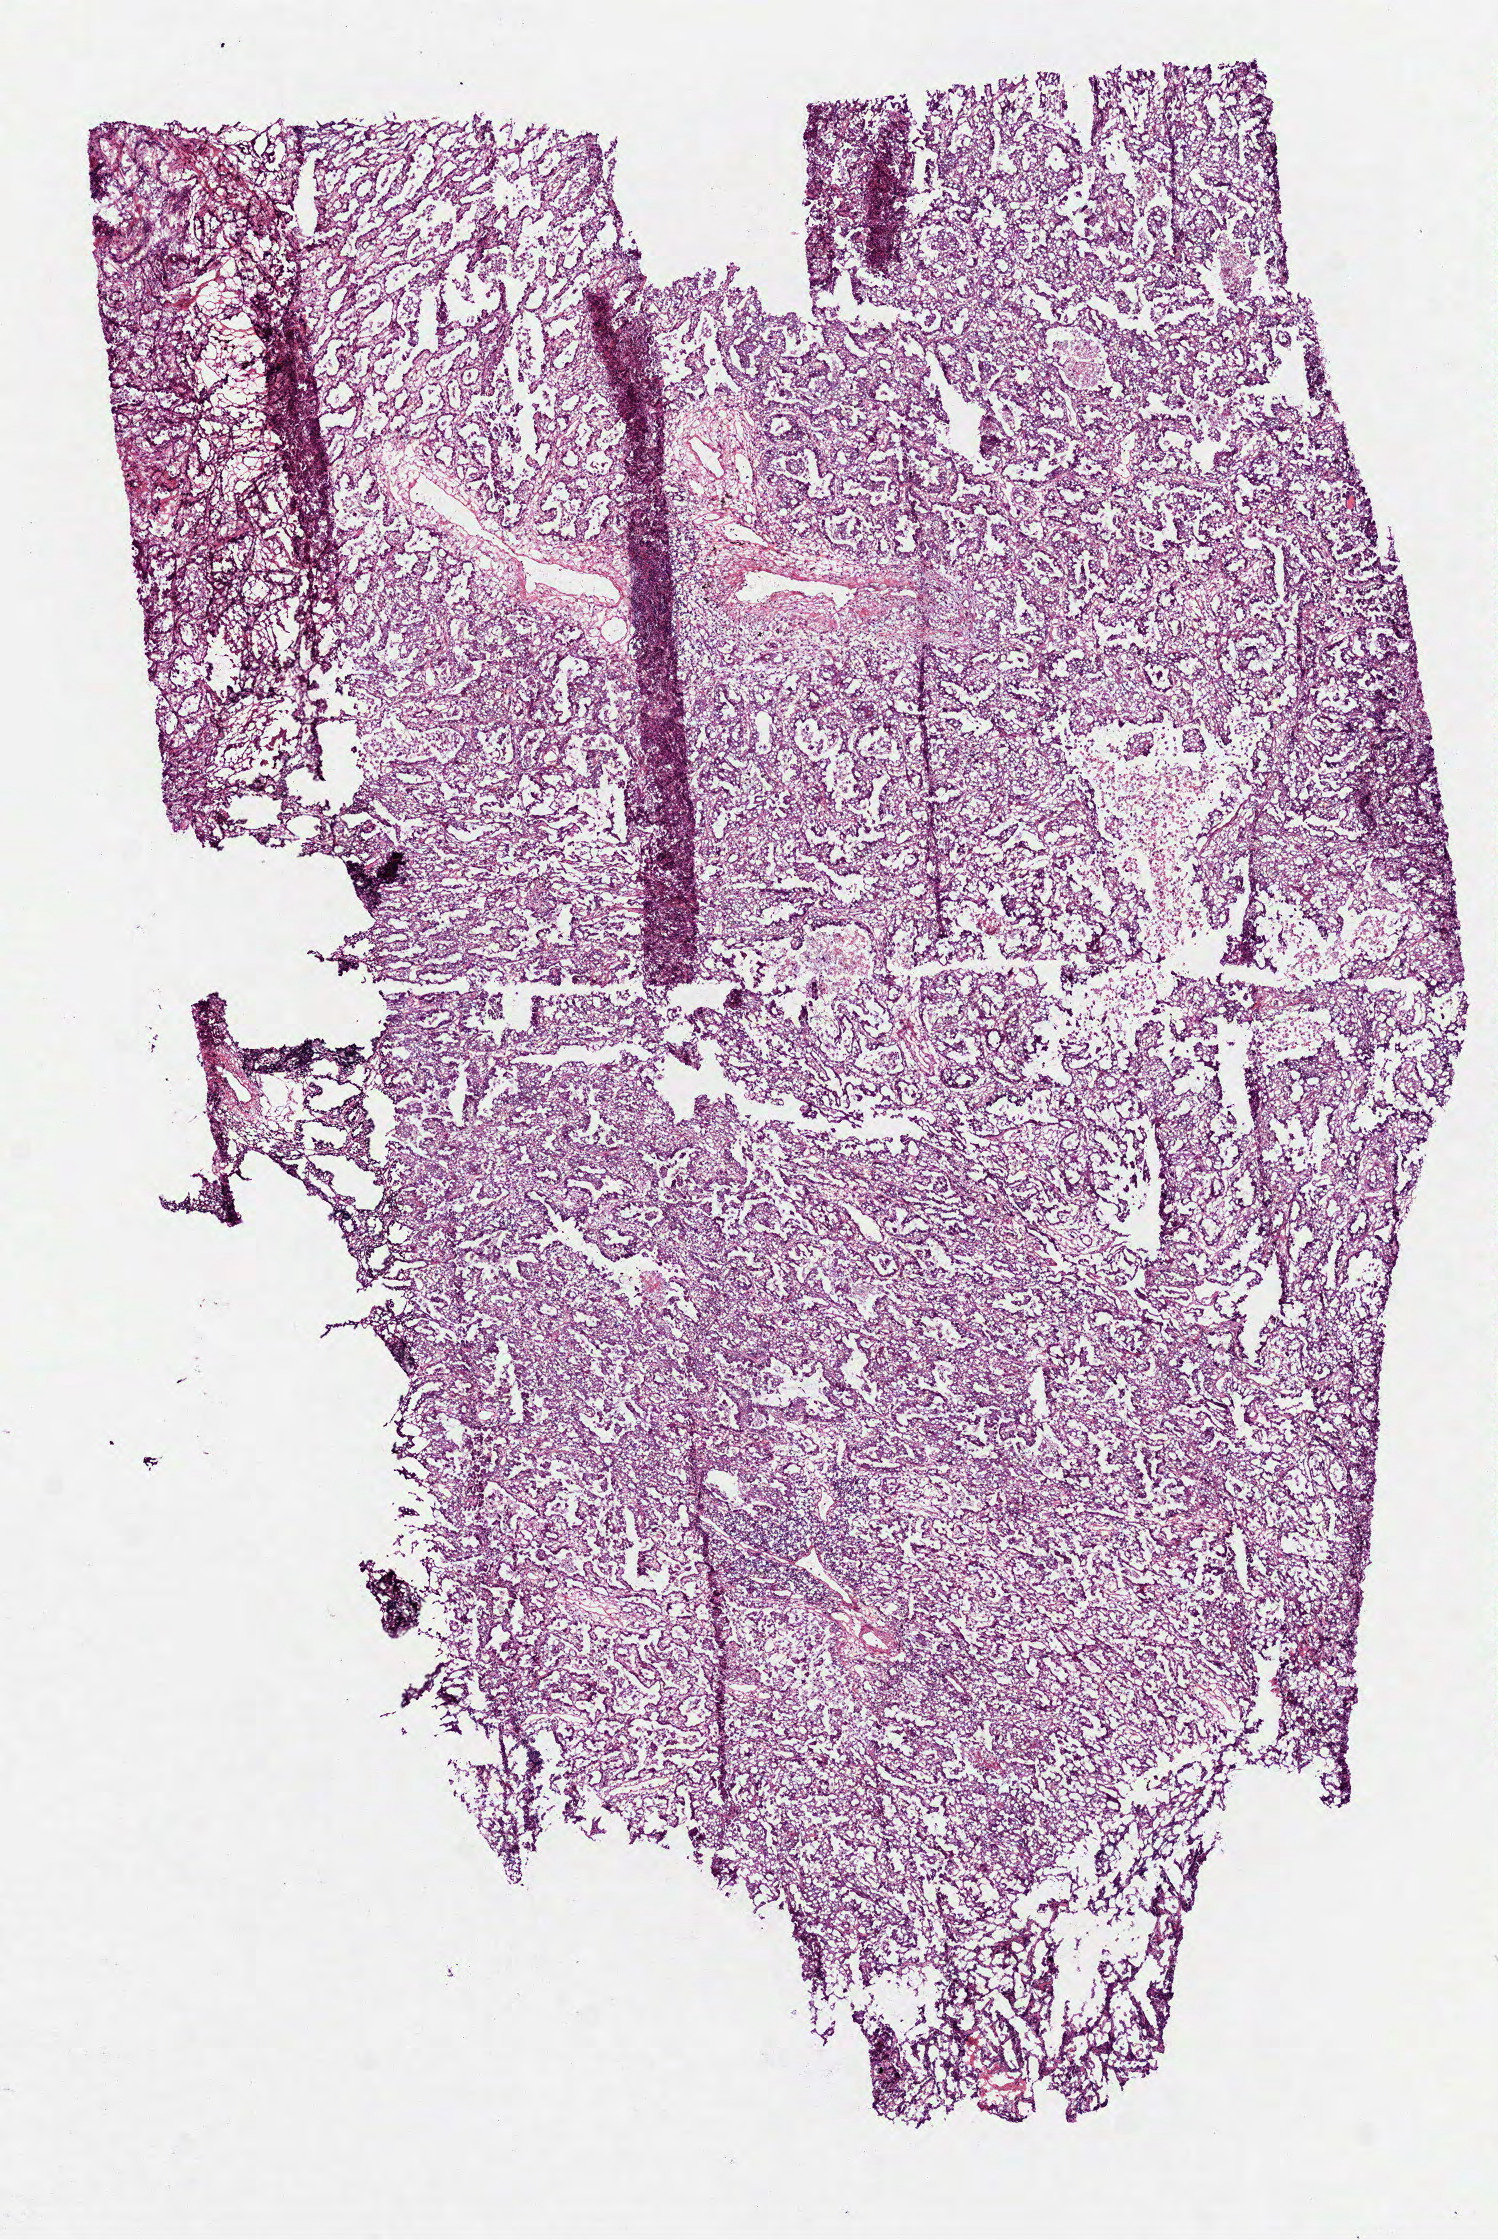
H&E whole-slide image, whole scanned area (about 6.0 x 9.0 mm) shown as a low-resolution overview; frozen section from the bottom of the tissue portion; sample: primary tumour, lung. Patient: female, age at initial diagnosis 62 years. Composition of this section per pathologist review: tumour cells 77%, tumour nuclei 70%, normal cells 5%, stromal cells 10%, necrosis 8%.
Histologic diagnosis: Bronchiolo-alveolar carcinoma, non-mucinous (upper lobe, lung). AJCC pathologic stage: IB (6th edition). TNM: T2 N0 M0.